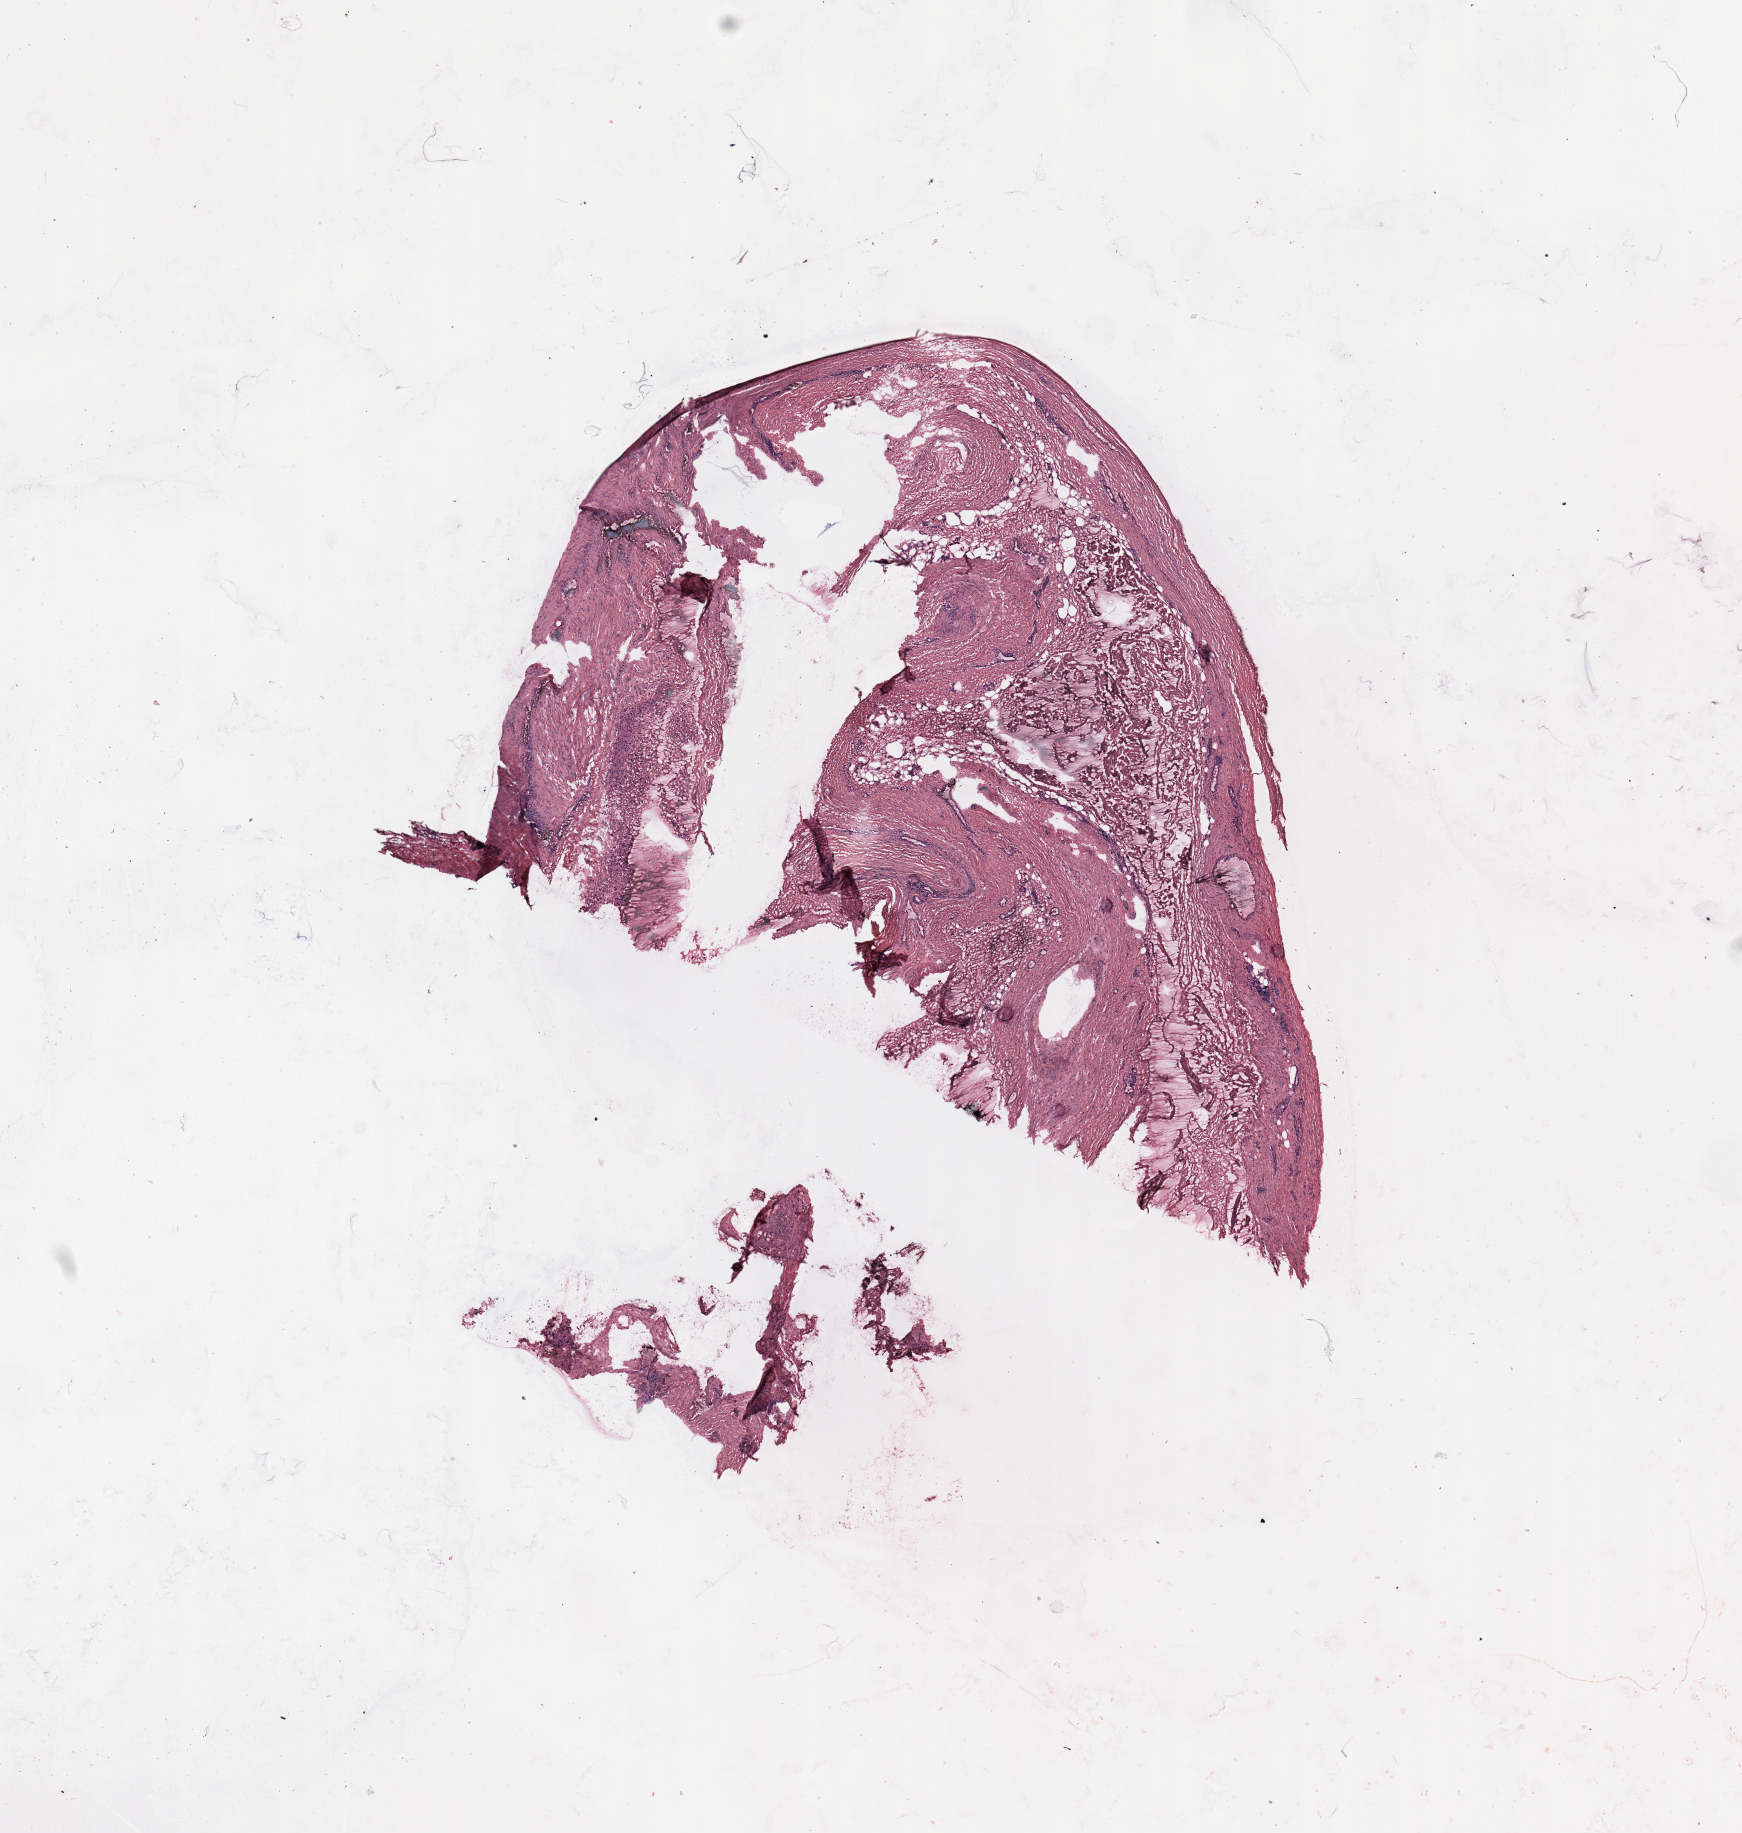
Digitized H&E-stained tissue section (whole slide) — whole scanned area (about 13.8 x 14.5 mm) shown as a low-resolution overview, normal (non-tumour) tissue sample. Male, 74 y/o.
This section: normal (non-tumour) tissue from the same patient. Patient diagnosis (cohort enrolment): sarcoma (site not recorded at cohort level).